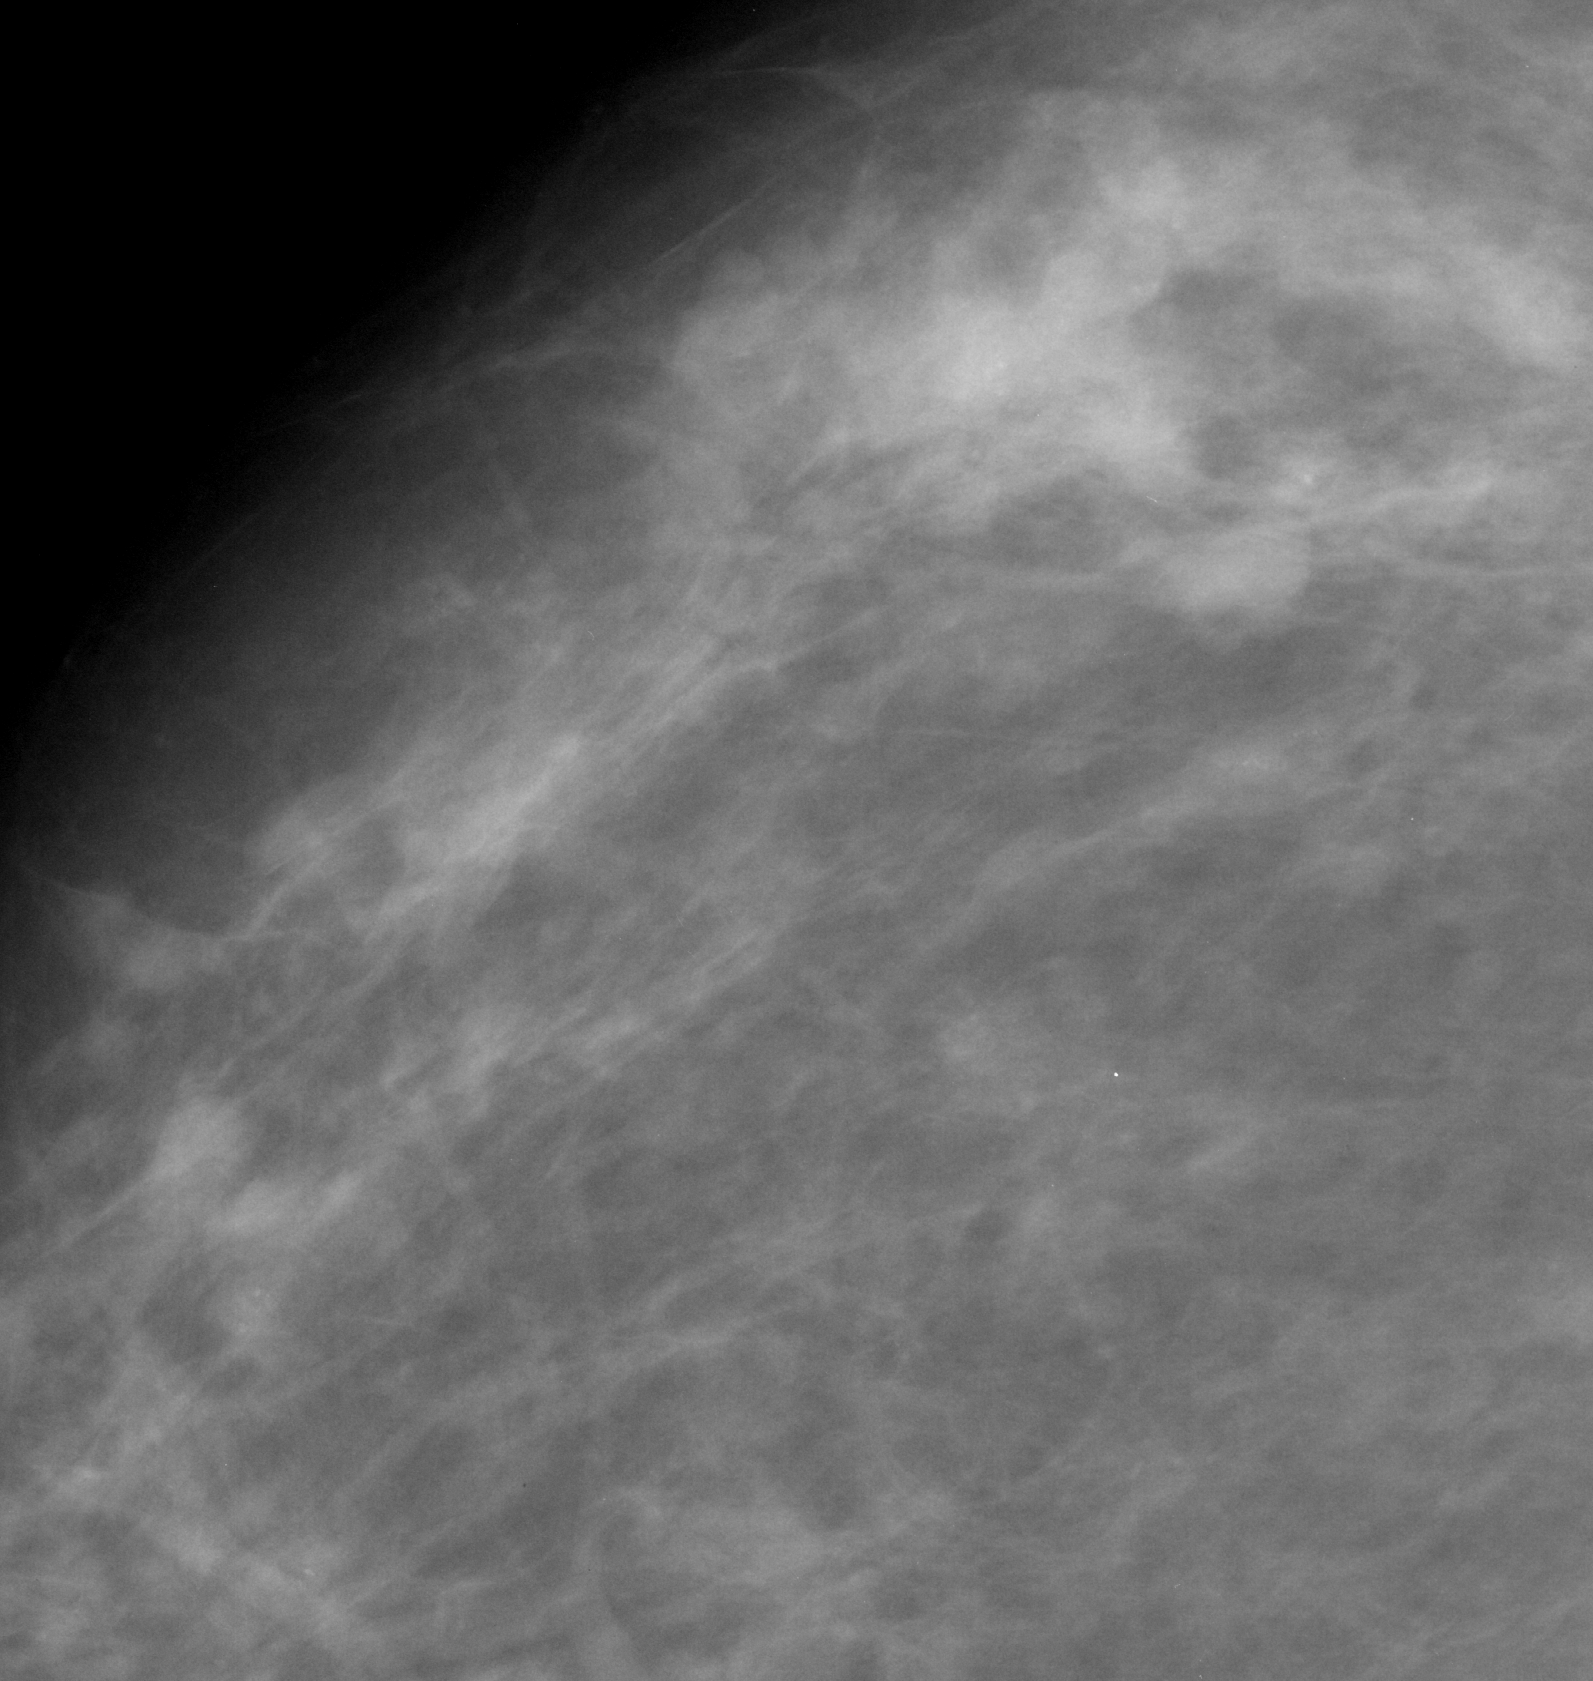
Cropped region of a digitized screen-film mammogram centred on a radiologist-marked abnormality; right breast; CC view.
Finding: calcifications, morphology amorphous, distribution regional; BI-RADS assessment category 4; pathology (as recorded): benign.